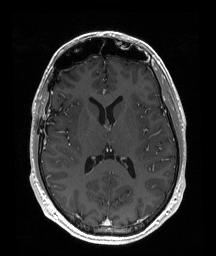
Brain MRI from a brain-tumour surgery series, one axial slice. Position 96 of 192 along the scan axis. T1-weighted post-contrast. 1 mm slice thickness. 216 × 256 image matrix, field of view 219 × 260 mm. From the clinical record (not read from this slice): histopathology: Astrocytoma; WHO grade: 2; IDH mutation: yes.
Annotated regions visible in this slice (expert manual segmentation):
- tumour: bounding box <68,108,80,125> (left, top, right, bottom; pixels)